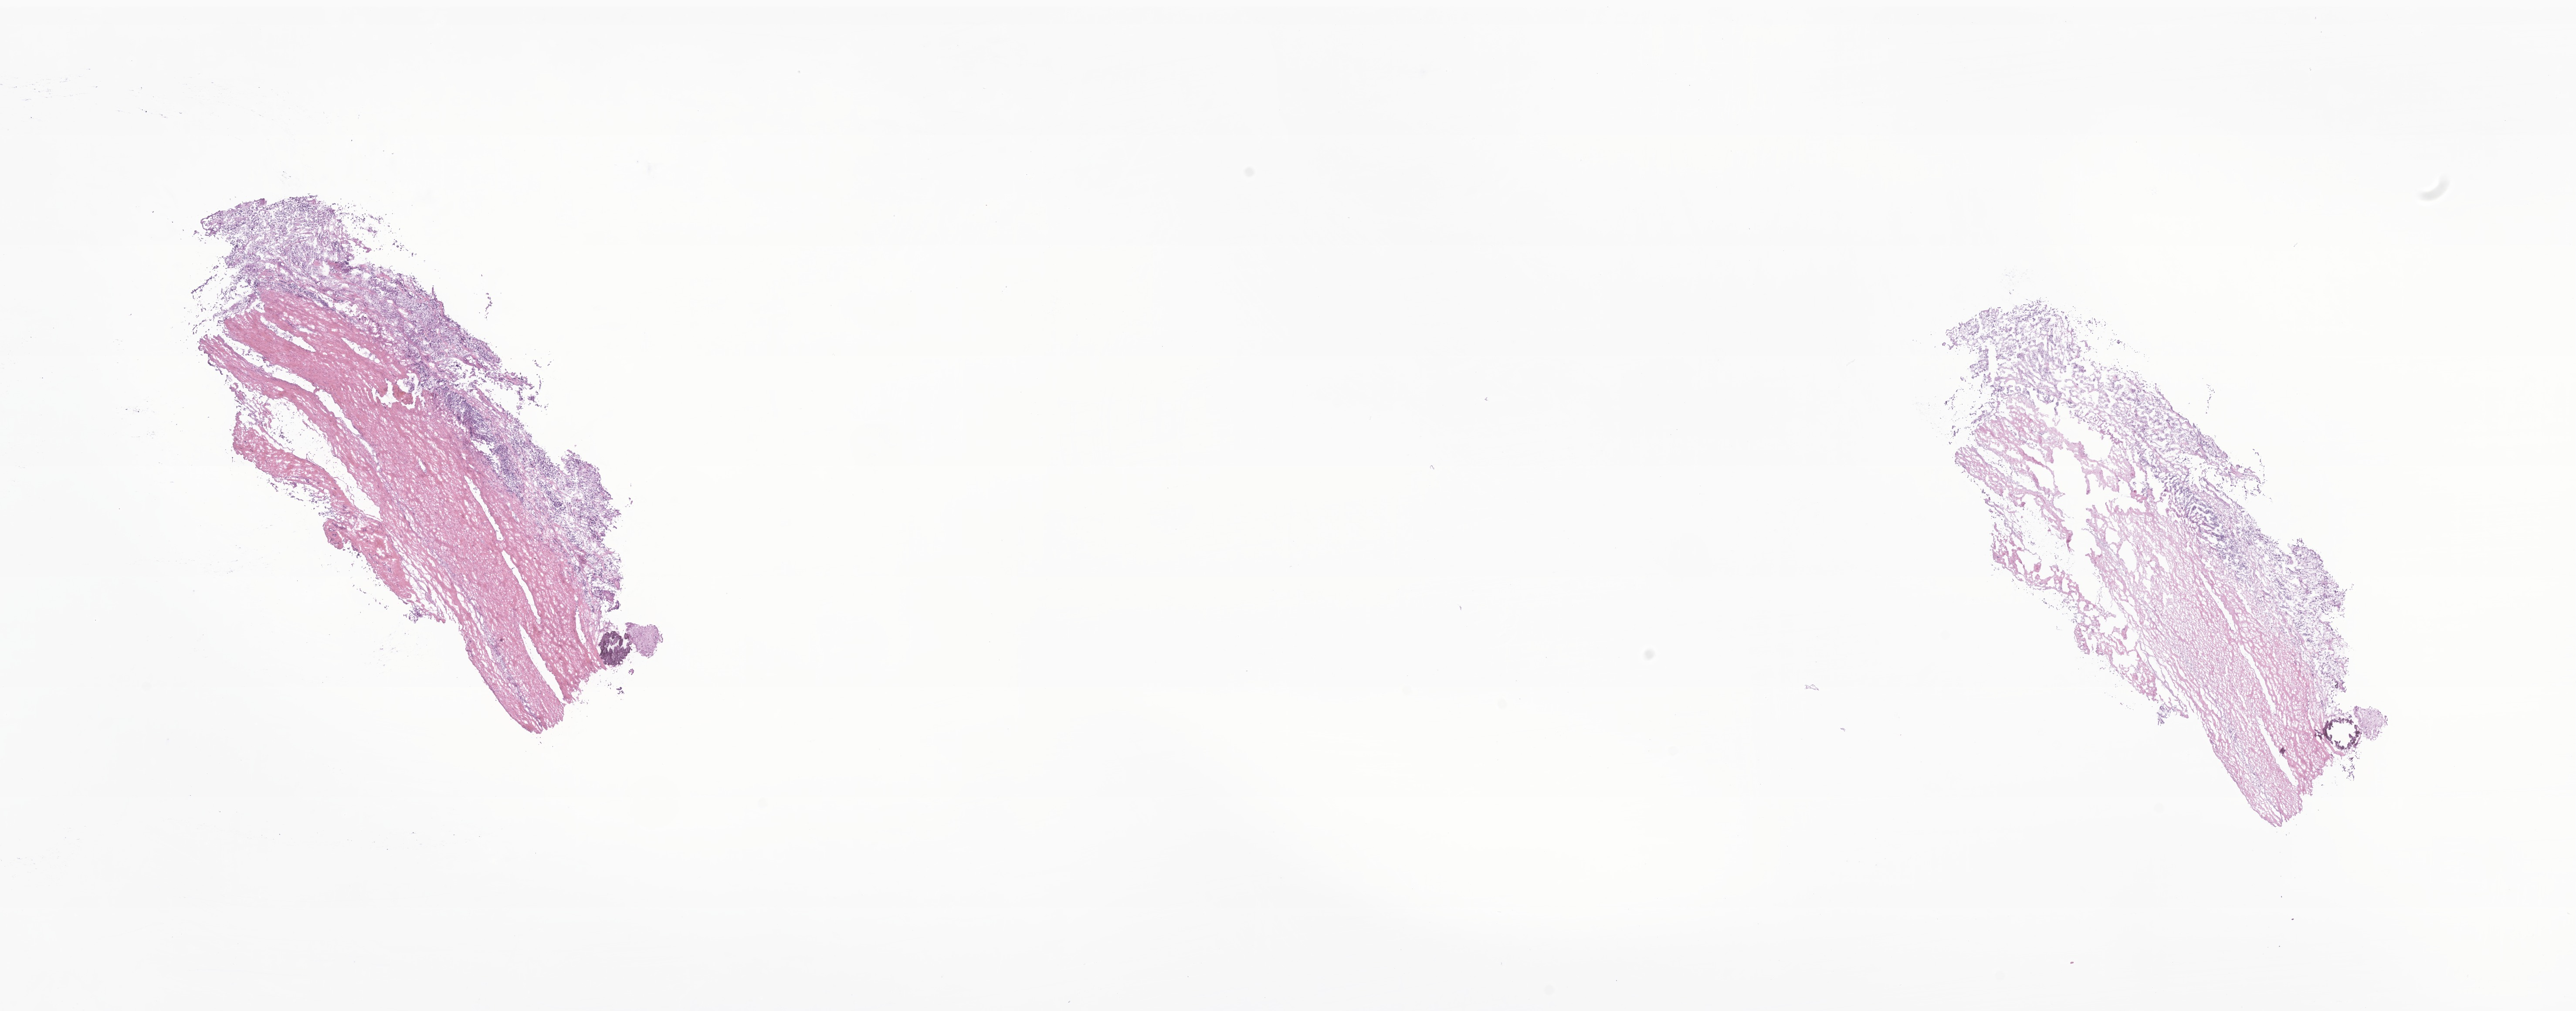
Hematoxylin and eosin (H&E) whole-slide image of tumor tissue from the adrenal gland, a low-resolution overview of the entire scanned area, about 24.9 x 9.8 mm; frozen section (OCT-embedded). Patient: female, age 796 days.
Diagnosis: Neuroblastoma, NOS.